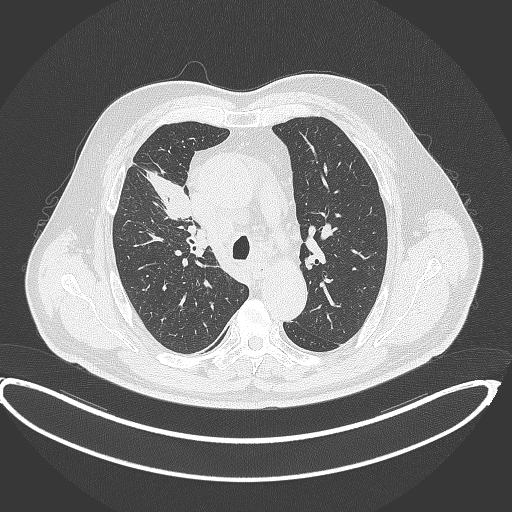
Chest CT, one axial slice. Position 283 of 390 along the scan axis. Reconstruction kernel B70f. 120 kVp. Lung window (W 1500 / L -600 HU). 1 mm slice thickness. 512 × 512 image matrix. Male patient, age 62 years. From the clinical record (not read from this slice): clinical TNM (as recorded): T1c N3 M1c.
Structures marked on this image (bounding box drawn by a radiologist):
- lung tumour (recorded histology: adenocarcinoma): box from (x=143, y=169) to (x=197, y=221) px